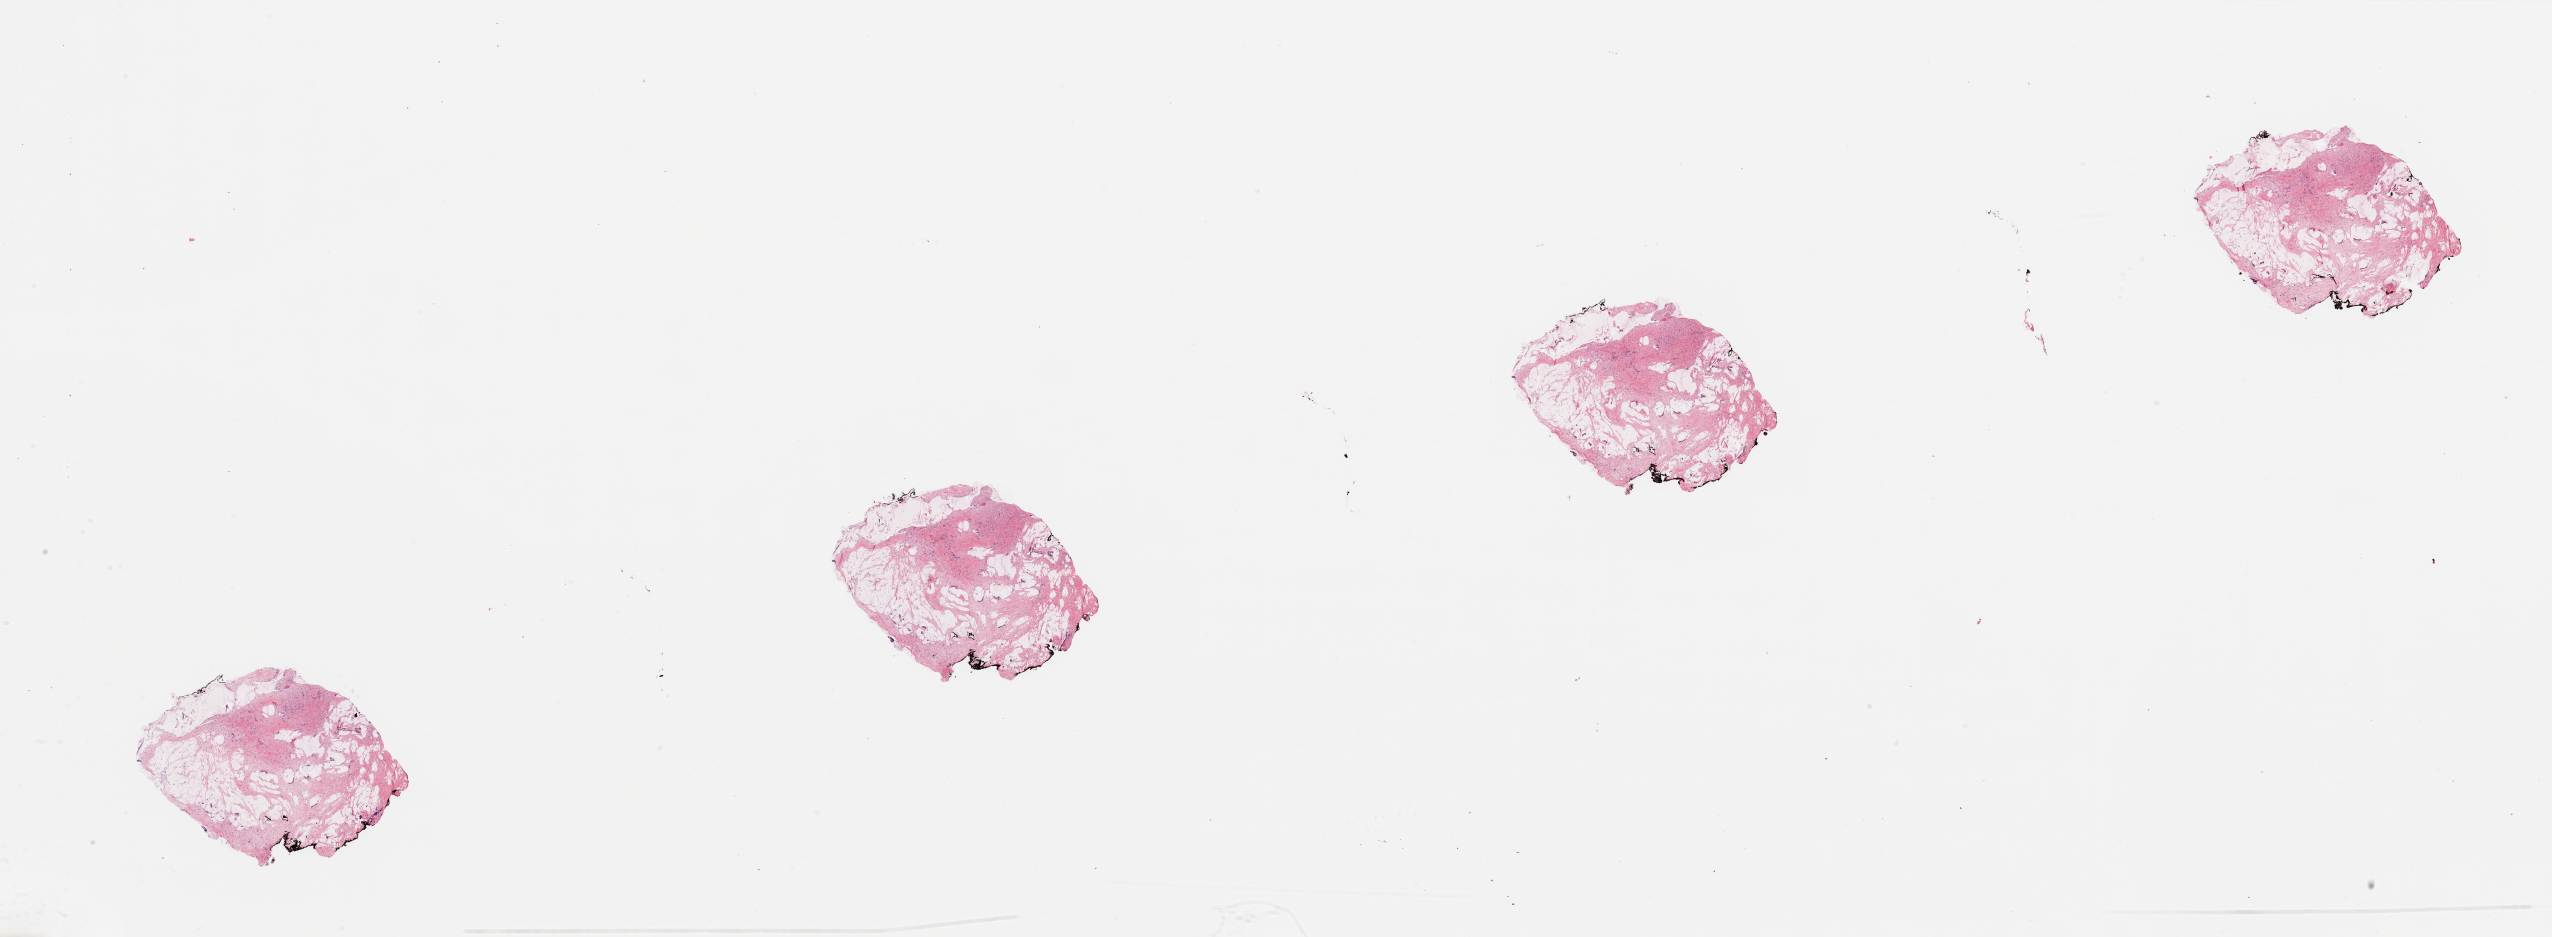
Whole-slide histology image, Hematoxylin and eosin (H&E) stained — whole scanned area (about 40.4 x 14.8 mm, acquisition: 20x scan) shown as a low-resolution overview; pancreas, tumour tissue. 63-year-old male patient.
Patient diagnosis (cohort enrolment): ductal adenocarcinoma (pancreas). Primary tumour site (as recorded): head.